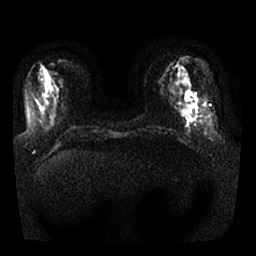
Breast MRI, one axial slice; position 7 of 25 along the scan axis; diffusion-weighted series; image 2 of 4 stored at this slice position (different b-values; order by instance number); 1.5 T; 4 mm slice thickness; 256 × 256 image matrix, field of view 330 × 330 mm. Female patient.
Annotated regions visible in this slice (outlined manually by an expert reader):
- tumour on diffusion-weighted imaging: bounding box <185,92,190,99> (left, top, right, bottom; pixels)